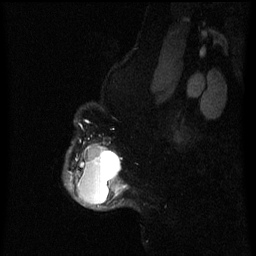
Breast MRI (dynamic contrast-enhanced), one sagittal slice. Position 53 of 60 along the scan axis. Dynamic contrast-enhanced series, image 2 of 3 at this slice position (ordered by acquisition). 1.5 T. TE 4.2 ms, TR 8 ms. 2 mm slice thickness. 256 × 256 image matrix. Patient: female, 50 years.
Annotated regions visible in this slice (semi-automatic segmentation, software-assisted and operator-edited):
- analysis volume of interest (the breast-tissue region the enhancement analysis was run in; not a lesion): box from (x=64, y=141) to (x=128, y=210) px
- tumour enhancement mask (voxels above the 70 % enhancement threshold inside the analysis volume of interest): (x=69, y=146)–(x=127, y=207)